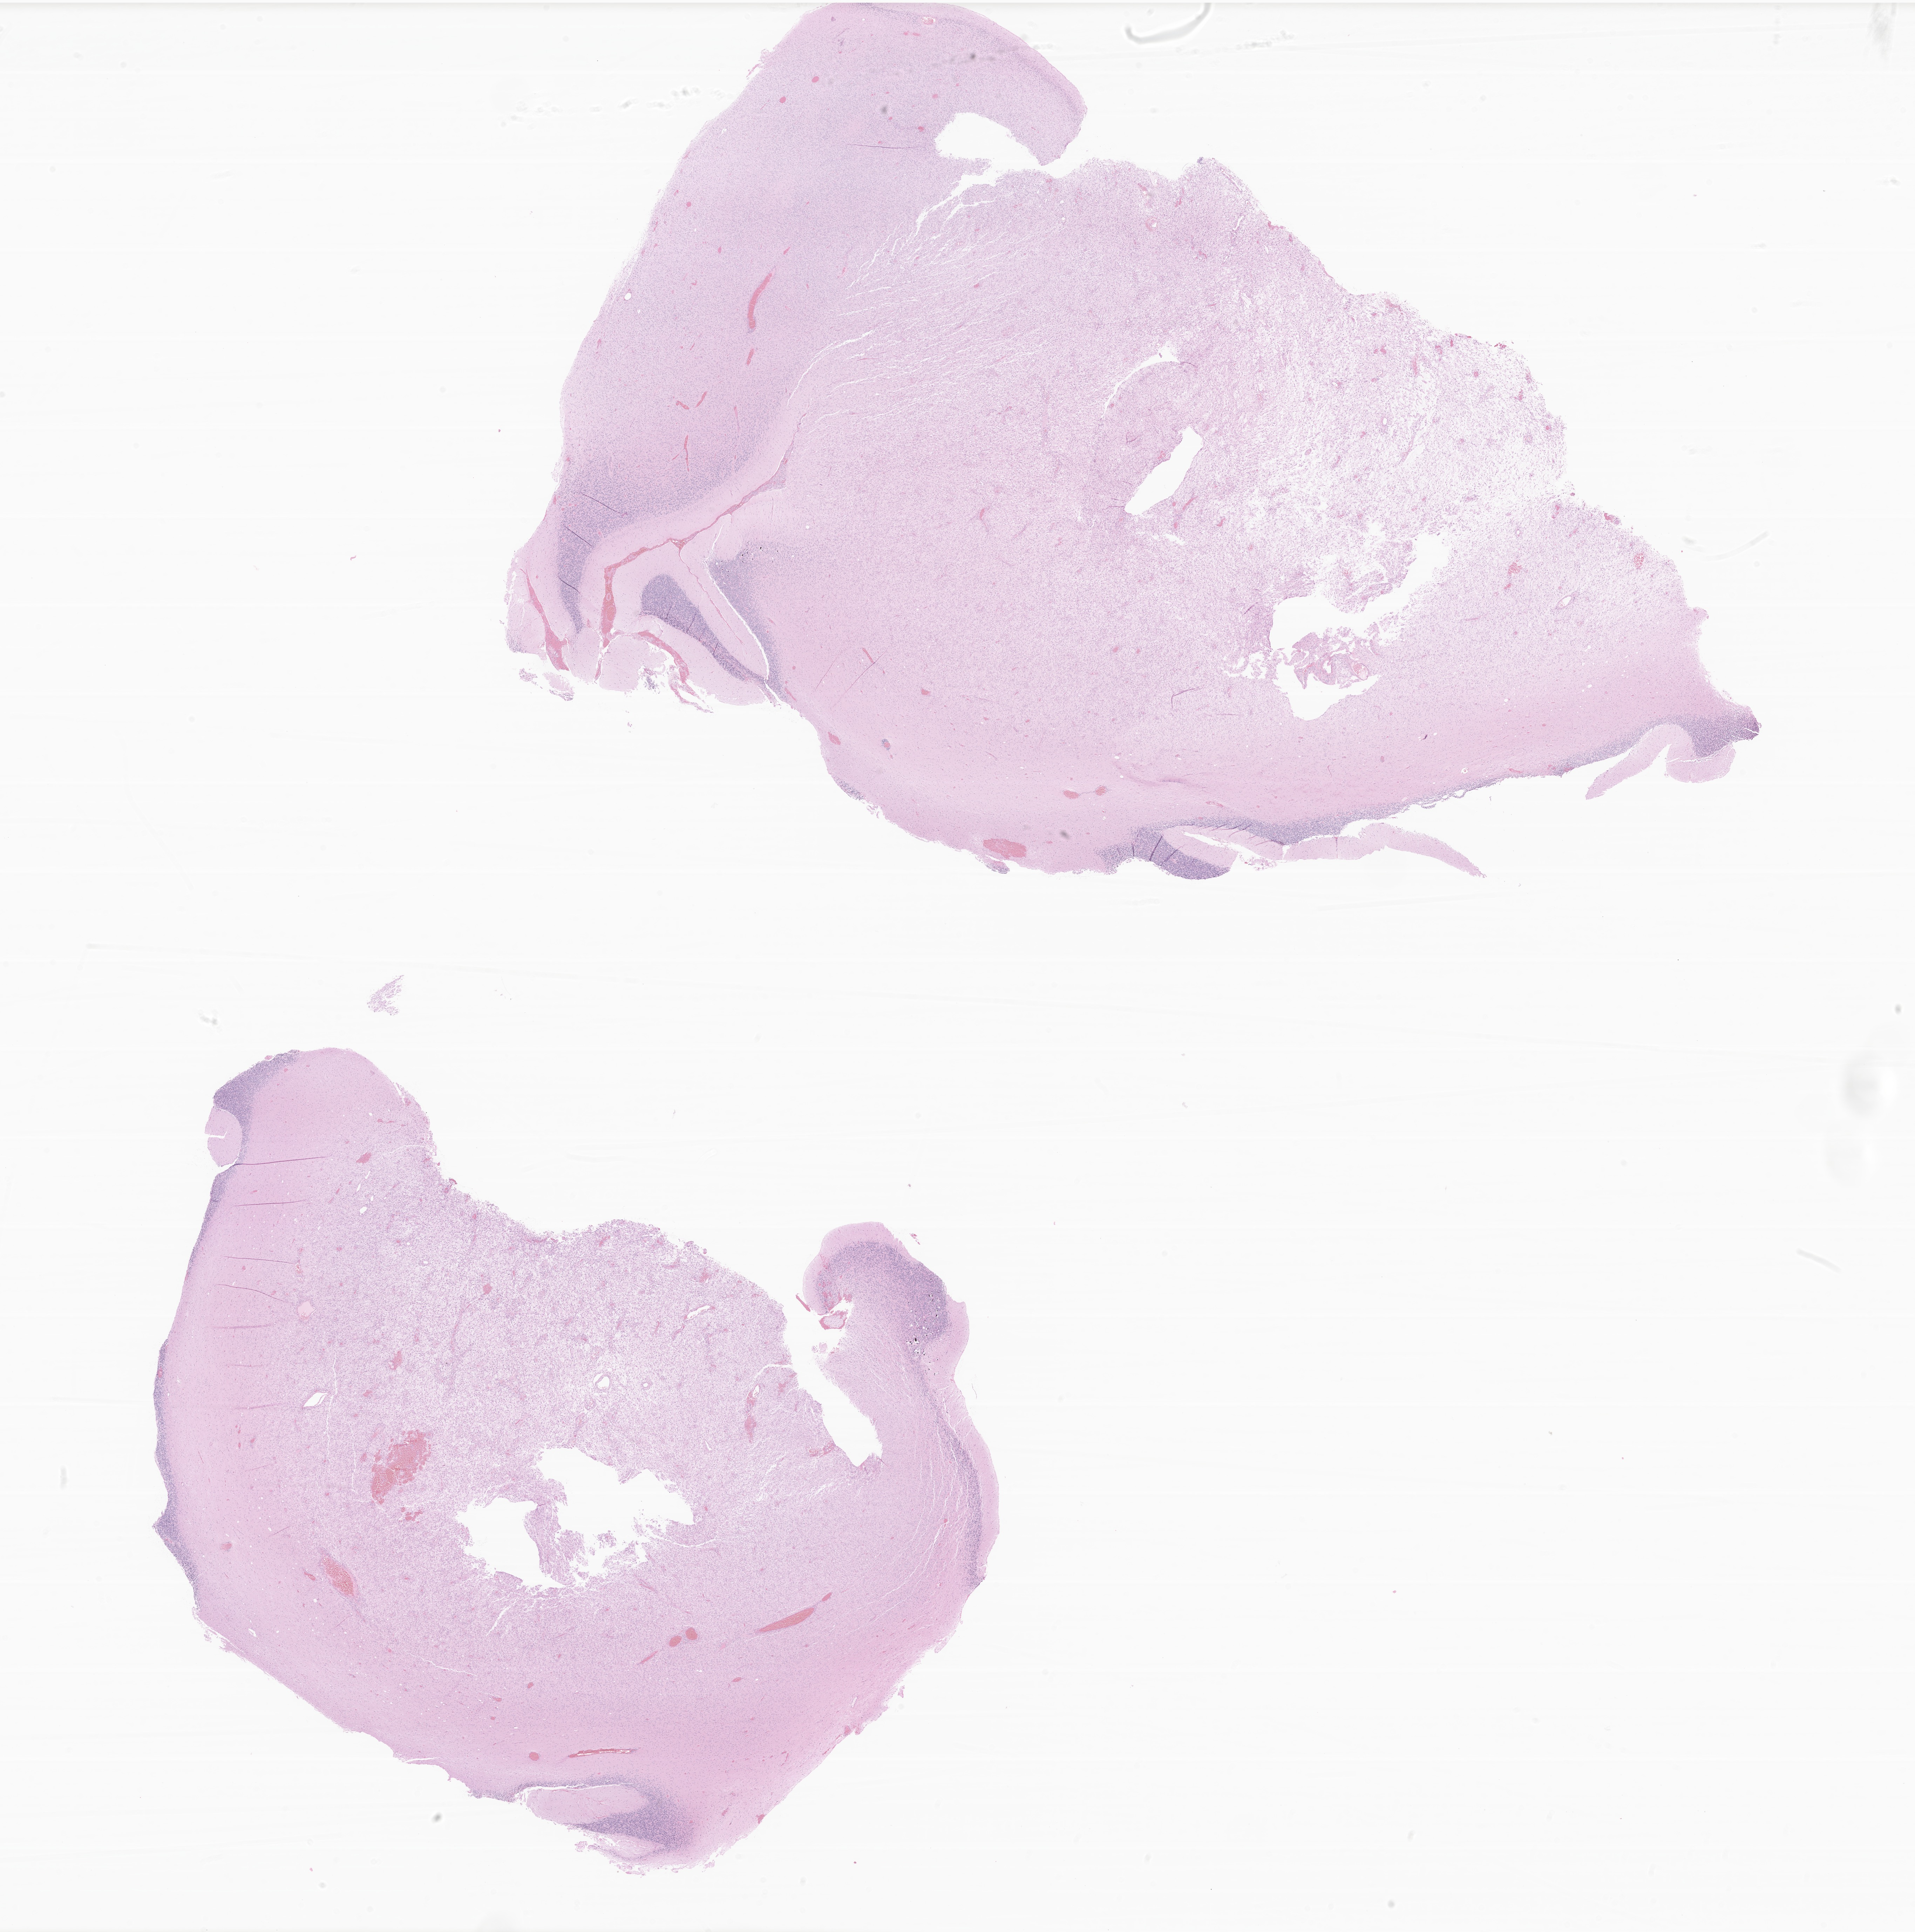
Whole-slide image, hematoxylin and eosin (H&E) stain of tumor tissue from the cerebellum, shown as a low-resolution overview of the whole scanned area (about 23.0 x 23.2 mm); formalin-fixed paraffin-embedded section. Male patient, age 165 months (13 years 9 months).
* recorded diagnosis: Pilocytic astrocytoma